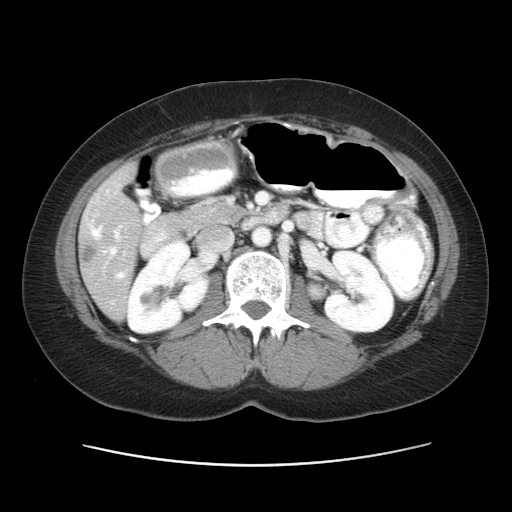
Contrast-enhanced abdominal CT, one axial slice; slice 23 of 52 in the series (ordered by position); 120 kVp; intravenous contrast given; soft-tissue window (W 400 / L 40 HU); 512 × 512 image matrix, field of view 362 × 362 mm. Female patient, age 48 years. Case-level facts recorded for this patient, not image findings: diagnosis: colorectal cancer liver metastases, imaged before liver resection; multiple liver metastases: yes; largest metastasis: 4.5 cm.
Annotated regions visible in this slice (outlined manually by an expert reader):
- hepatic veins: bounding box [x1, y1, x2, y2] px = [89, 222, 124, 278]
- liver: [79, 165, 142, 319]
- portal vein (with intrahepatic branches): [109, 230, 120, 256]
- liver metastasis: [83, 245, 97, 265]